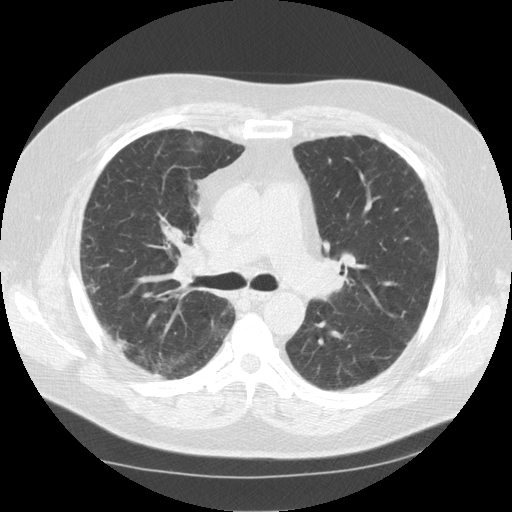
Low-dose screening chest CT, axial slice. Third screening round (two years after baseline). Lung window (W 1500 / L -600 HU). 2.5 mm slice thickness. Standard (soft-tissue) reconstruction kernel (STANDARD). Slice 44 of 112 in the series. Male, age 56 years at enrolment. Current smoker at enrolment.
- Lesion marked by an expert reader, bounding box <100,322,143,363> (left, top, right, bottom; pixels).
- The screening reader recorded 2 non-calcified nodules or masses ≥4 mm on this exam (right upper lobe, right lower lobe); which of them this box marks is not recorded.
- Official screen result: positive, other.
- Later outcome: lung cancer diagnosed 66 days after this screen — large cell neuroendocrine carcinoma, right upper lobe, stage IIIA (AJCC 6th edition), 10 mm at pathology.